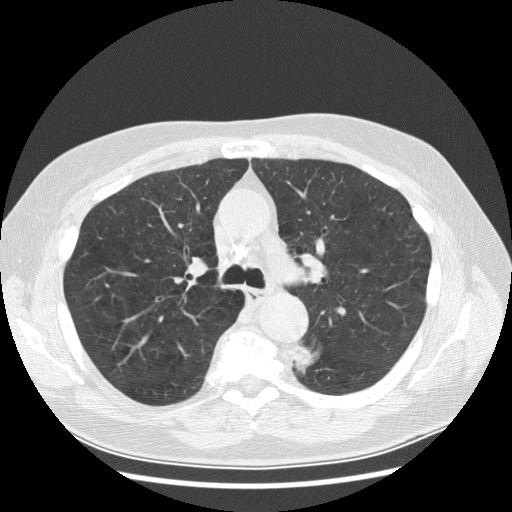
Low-dose screening chest CT, one axial slice; slice 190 of 282 in the series (ordered by position); reconstruction kernel STANDARD; lung window (W 1500 / L -600 HU); 2.5 mm slice thickness; 512 × 512 image matrix, field of view 370 × 370 mm.
Annotated regions visible in this slice (manually delineated by an expert):
- lesion 1 (tumor, lower lobe of left lung): box from (x=292, y=344) to (x=318, y=373) px